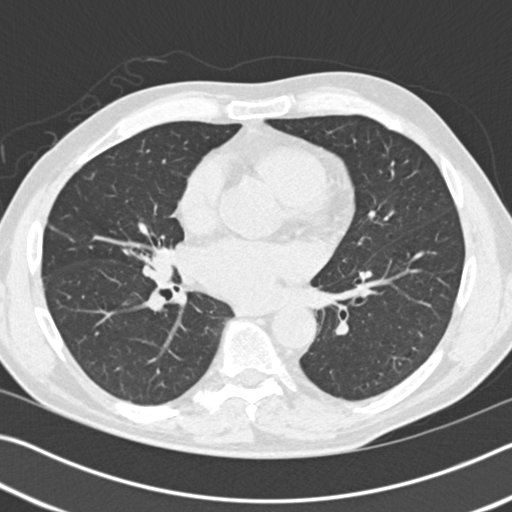
Axial slice from a low-dose chest CT screening exam, first (baseline) screen, lung window (W 1500 / L -600 HU), 2 mm slice thickness, standard (soft-tissue) reconstruction kernel (B30f), 120 kVp. Male participant, aged 57 years at enrolment.
• Expert-annotated lung lesion, bounding box [x1, y1, x2, y2] px = [142, 248, 179, 284].
• The screening reader recorded 2 non-calcified nodules or masses ≥4 mm on this exam (right middle lobe, right middle lobe); which of them this box marks is not recorded.
• Lung cancer was diagnosed 784 days after this screen (after the third annual screen): carcinoid tumor, NOS, right middle lobe, carcinoid, stage not assessed, 15 mm at pathology.